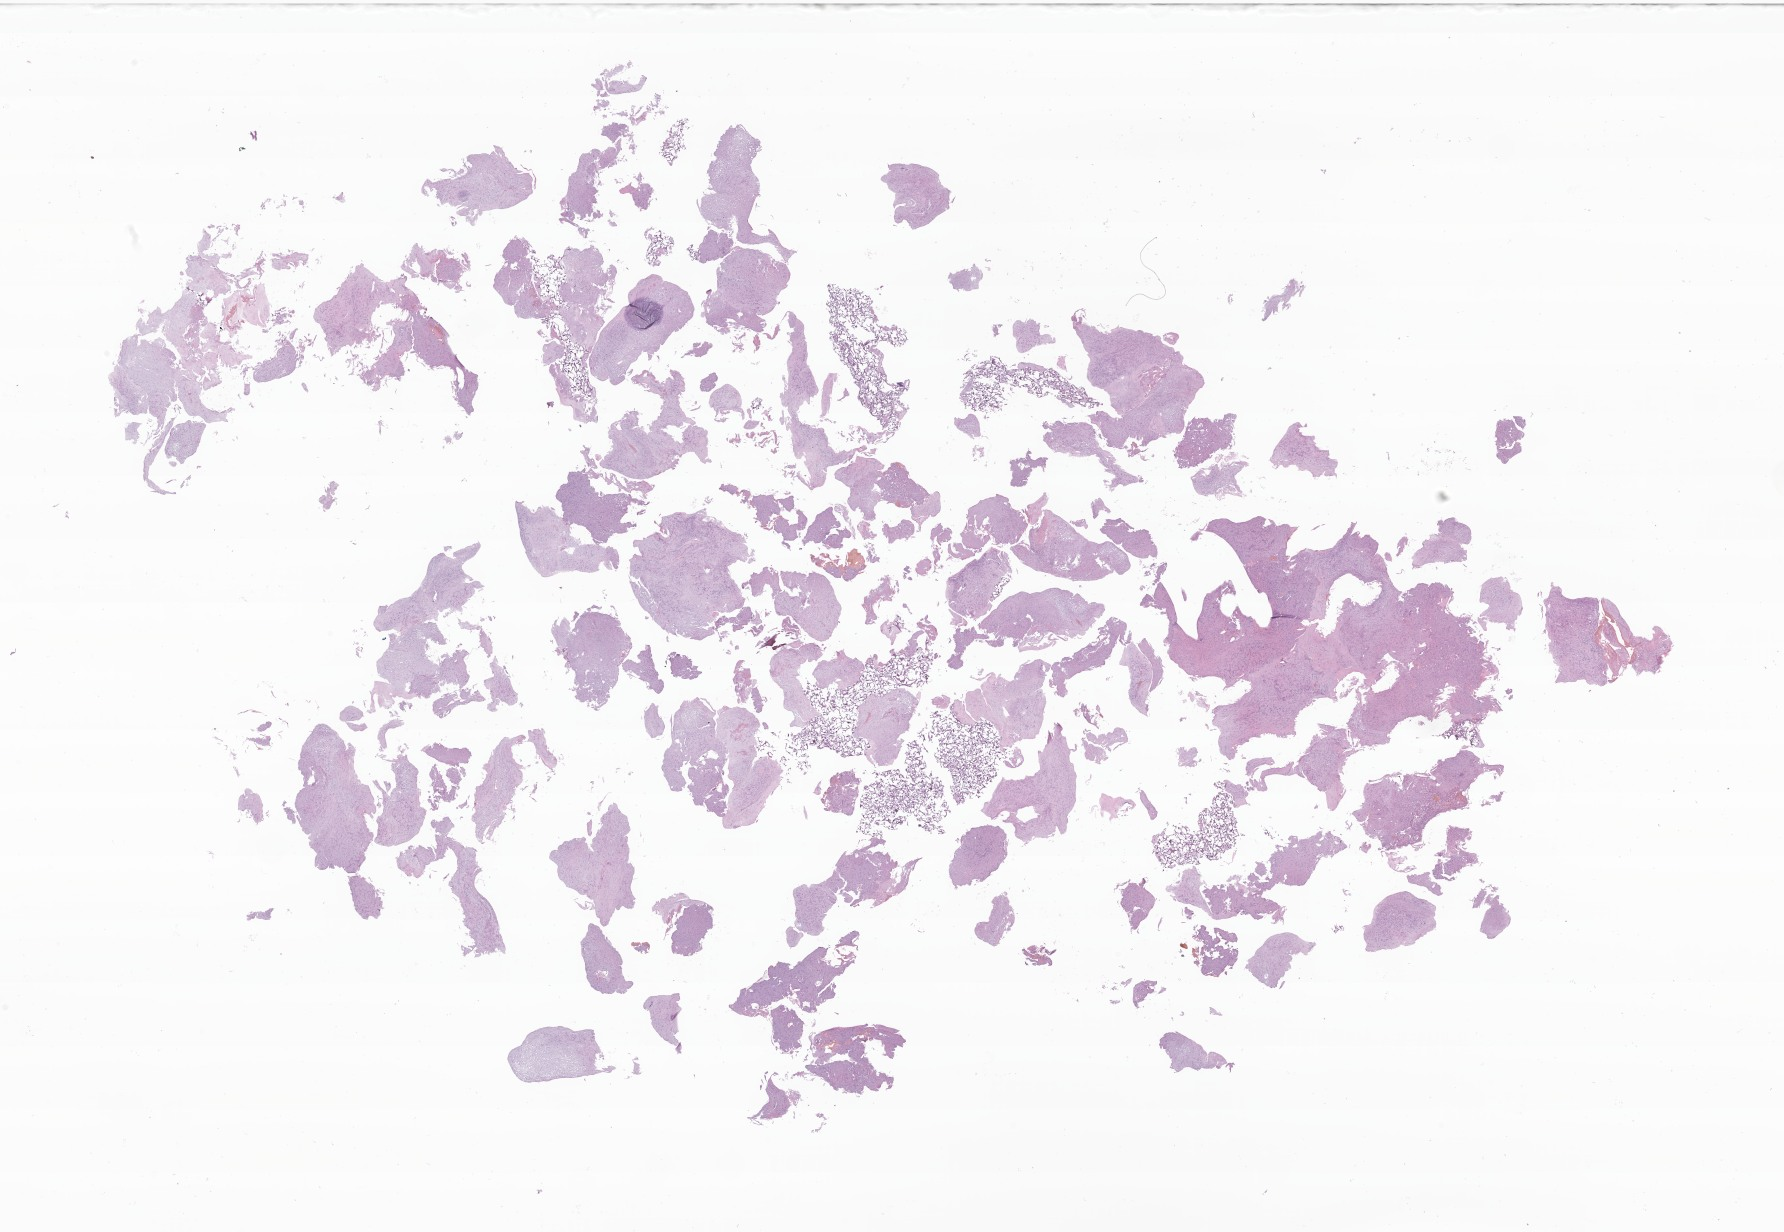
Whole-slide image, hematoxylin and eosin (H&E) stain of tumor tissue from the brain, a low-resolution overview of the entire scanned area, about 30.1 x 20.8 mm. Formalin-fixed, paraffin-embedded (FFPE) tissue. Patient: male, age 170 months (14 years 2 months).
- recorded diagnosis: Glioma, malignant